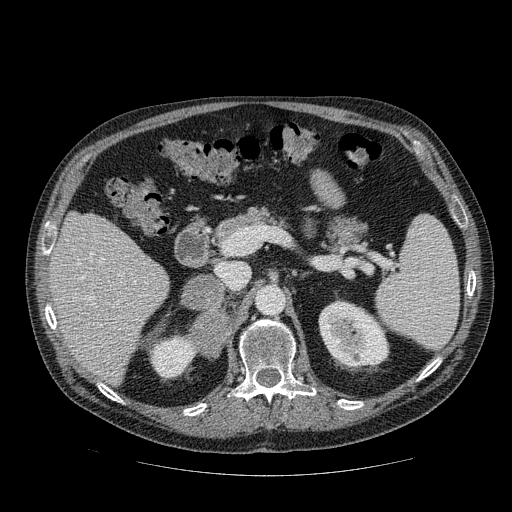
Contrast-enhanced abdominal CT, one axial slice; reconstruction kernel STANDARD; 120 kVp; intravenous contrast given; soft-tissue window (W 400 / L 40 HU); 512 × 512 image matrix, field of view 420 × 420 mm. Male patient, age 56 years. From the clinical record (not read from this slice): diagnosis: adrenocortical carcinoma; tumour side: right adrenal; tumour size at pathology: 9 cm; Ki-67 index: 48 %; stage (as recorded): 4.
Structures marked on this image (semi-automatically segmented with operator editing):
- mass: bounding box (x1, y1, x2, y2) in pixels: (183, 274, 231, 357)